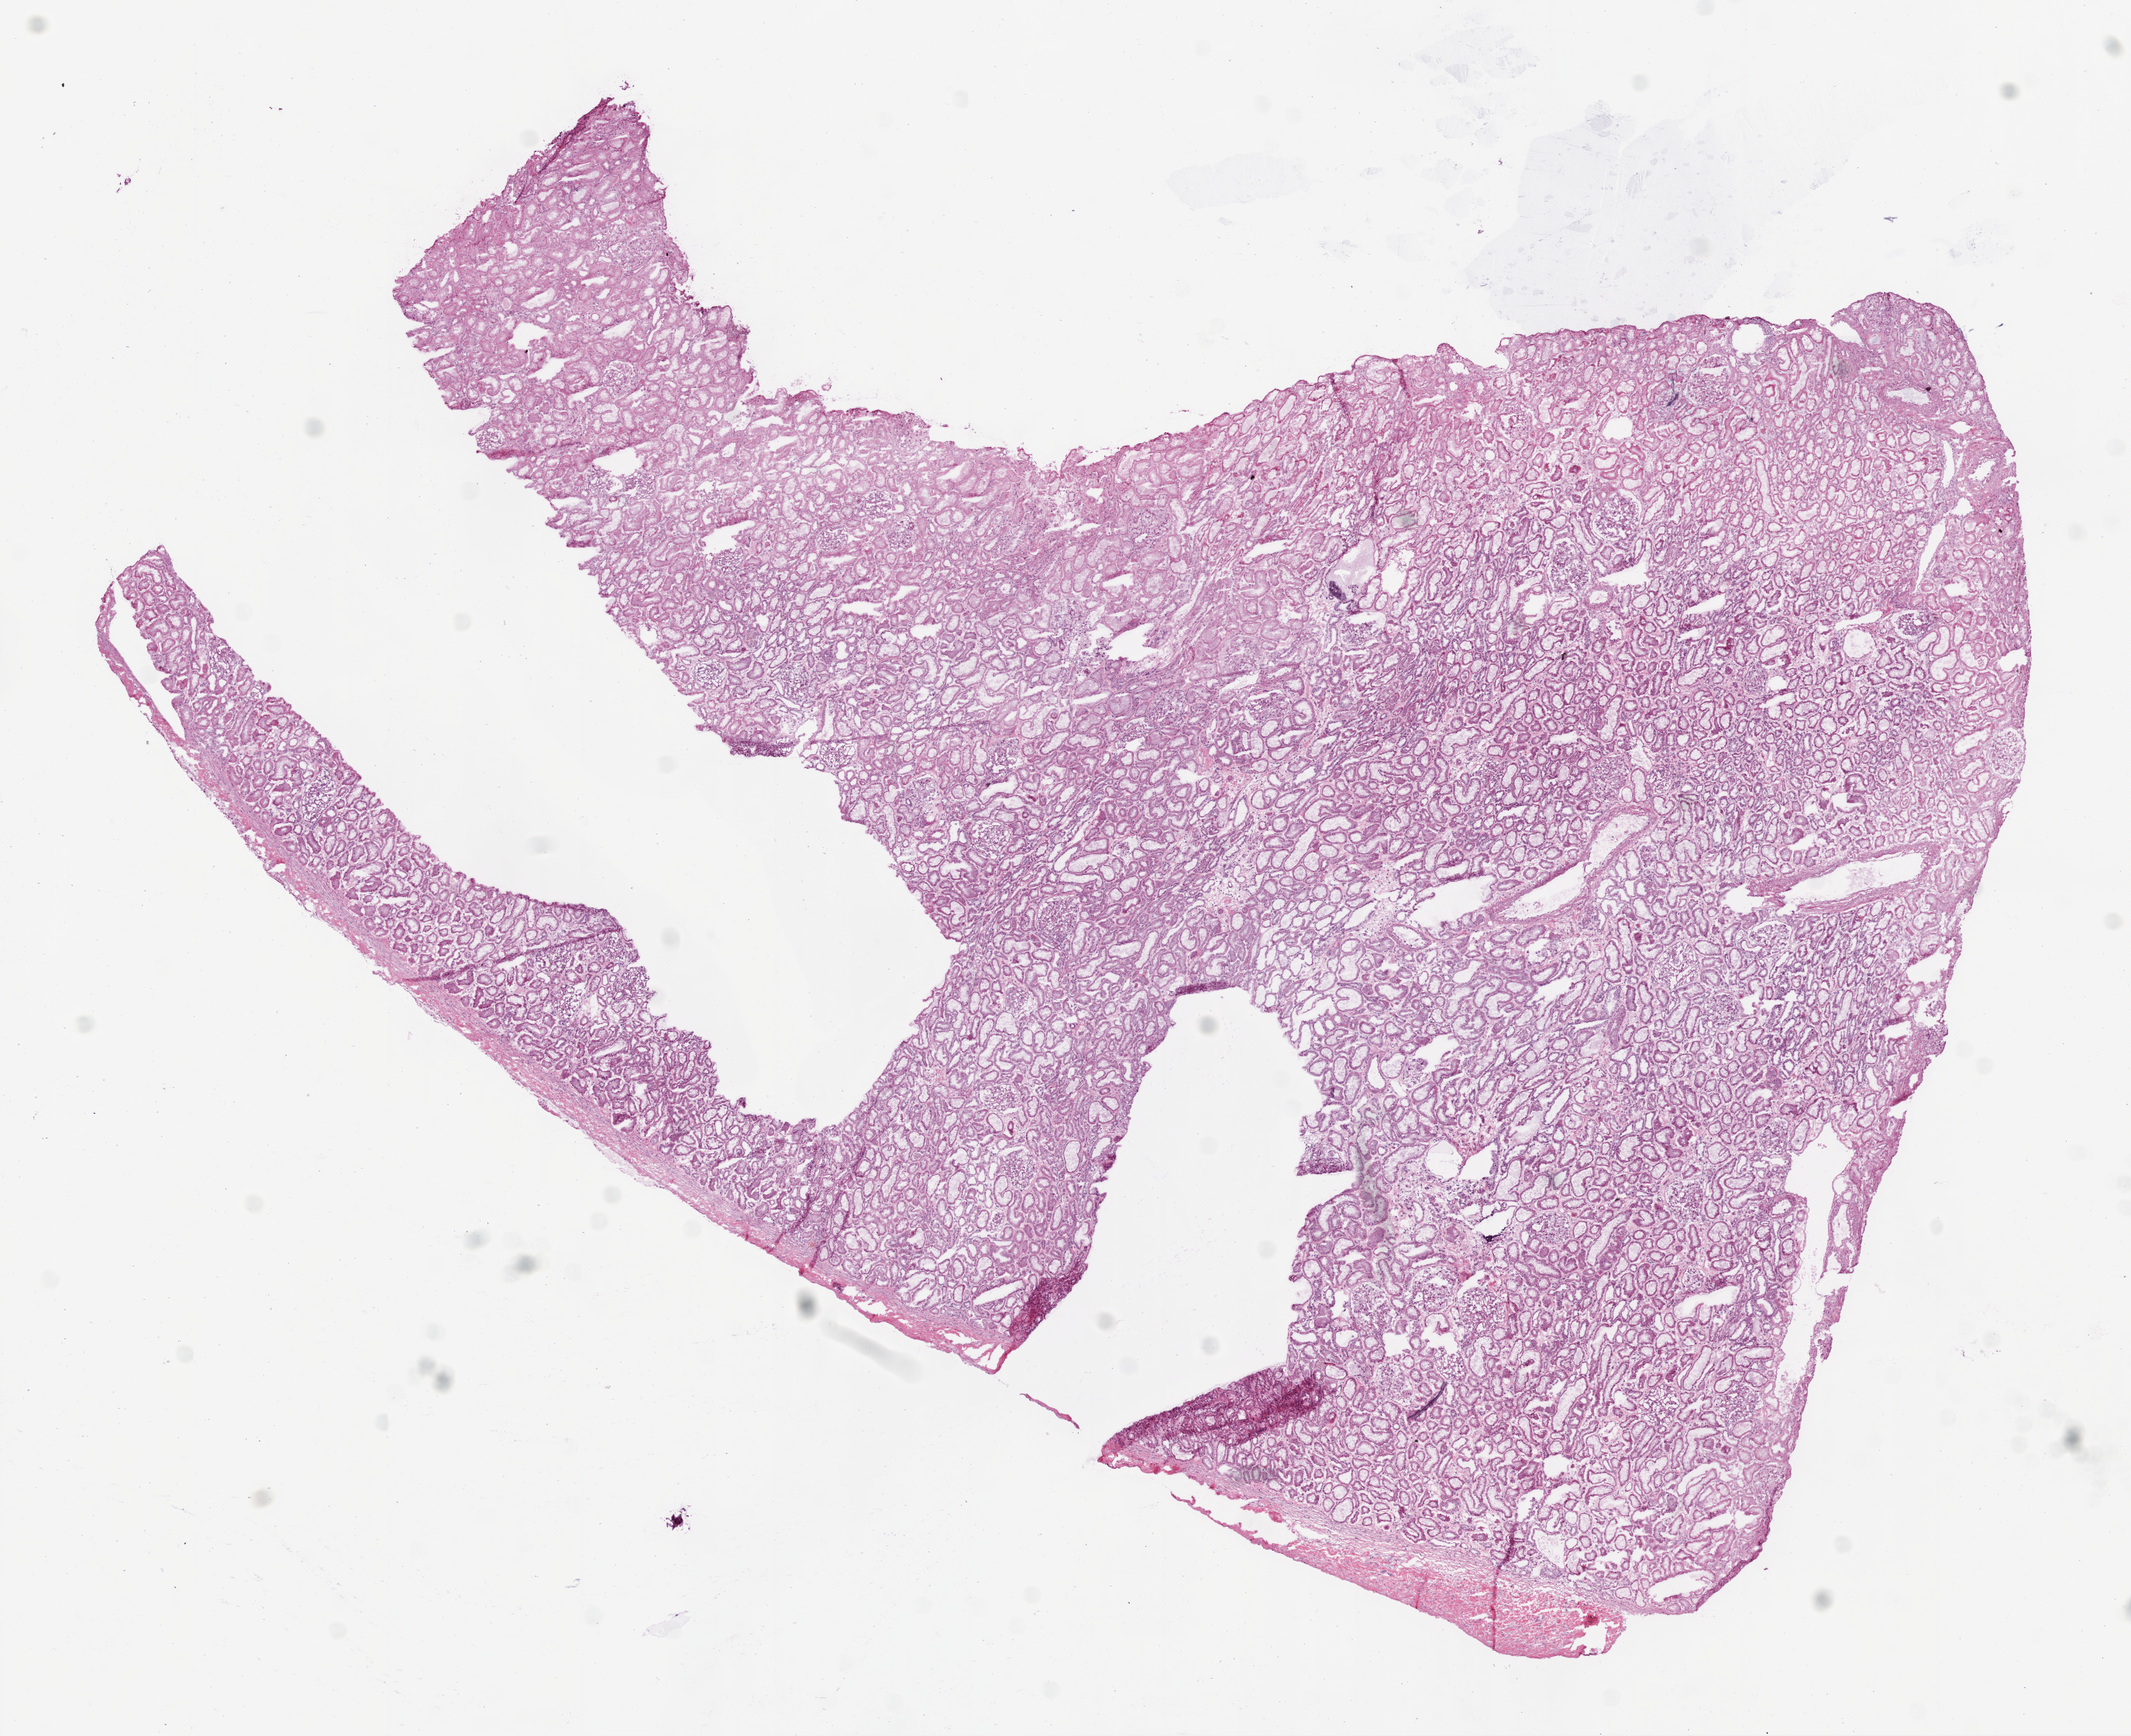
Digitized Hematoxylin and eosin (H&E) stained tissue section (whole slide), a low-resolution overview of the entire scanned area, about 11.0 x 9.0 mm (acquisition: 20x scan). Frozen section from the bottom of the tissue portion. Sample: solid tissue normal (non-tumour tissue), kidney. Male, age 64 years at initial diagnosis.
This section: solid tissue normal (non-tumour) sample from the same patient. Patient diagnosis: Clear cell adenocarcinoma, NOS.